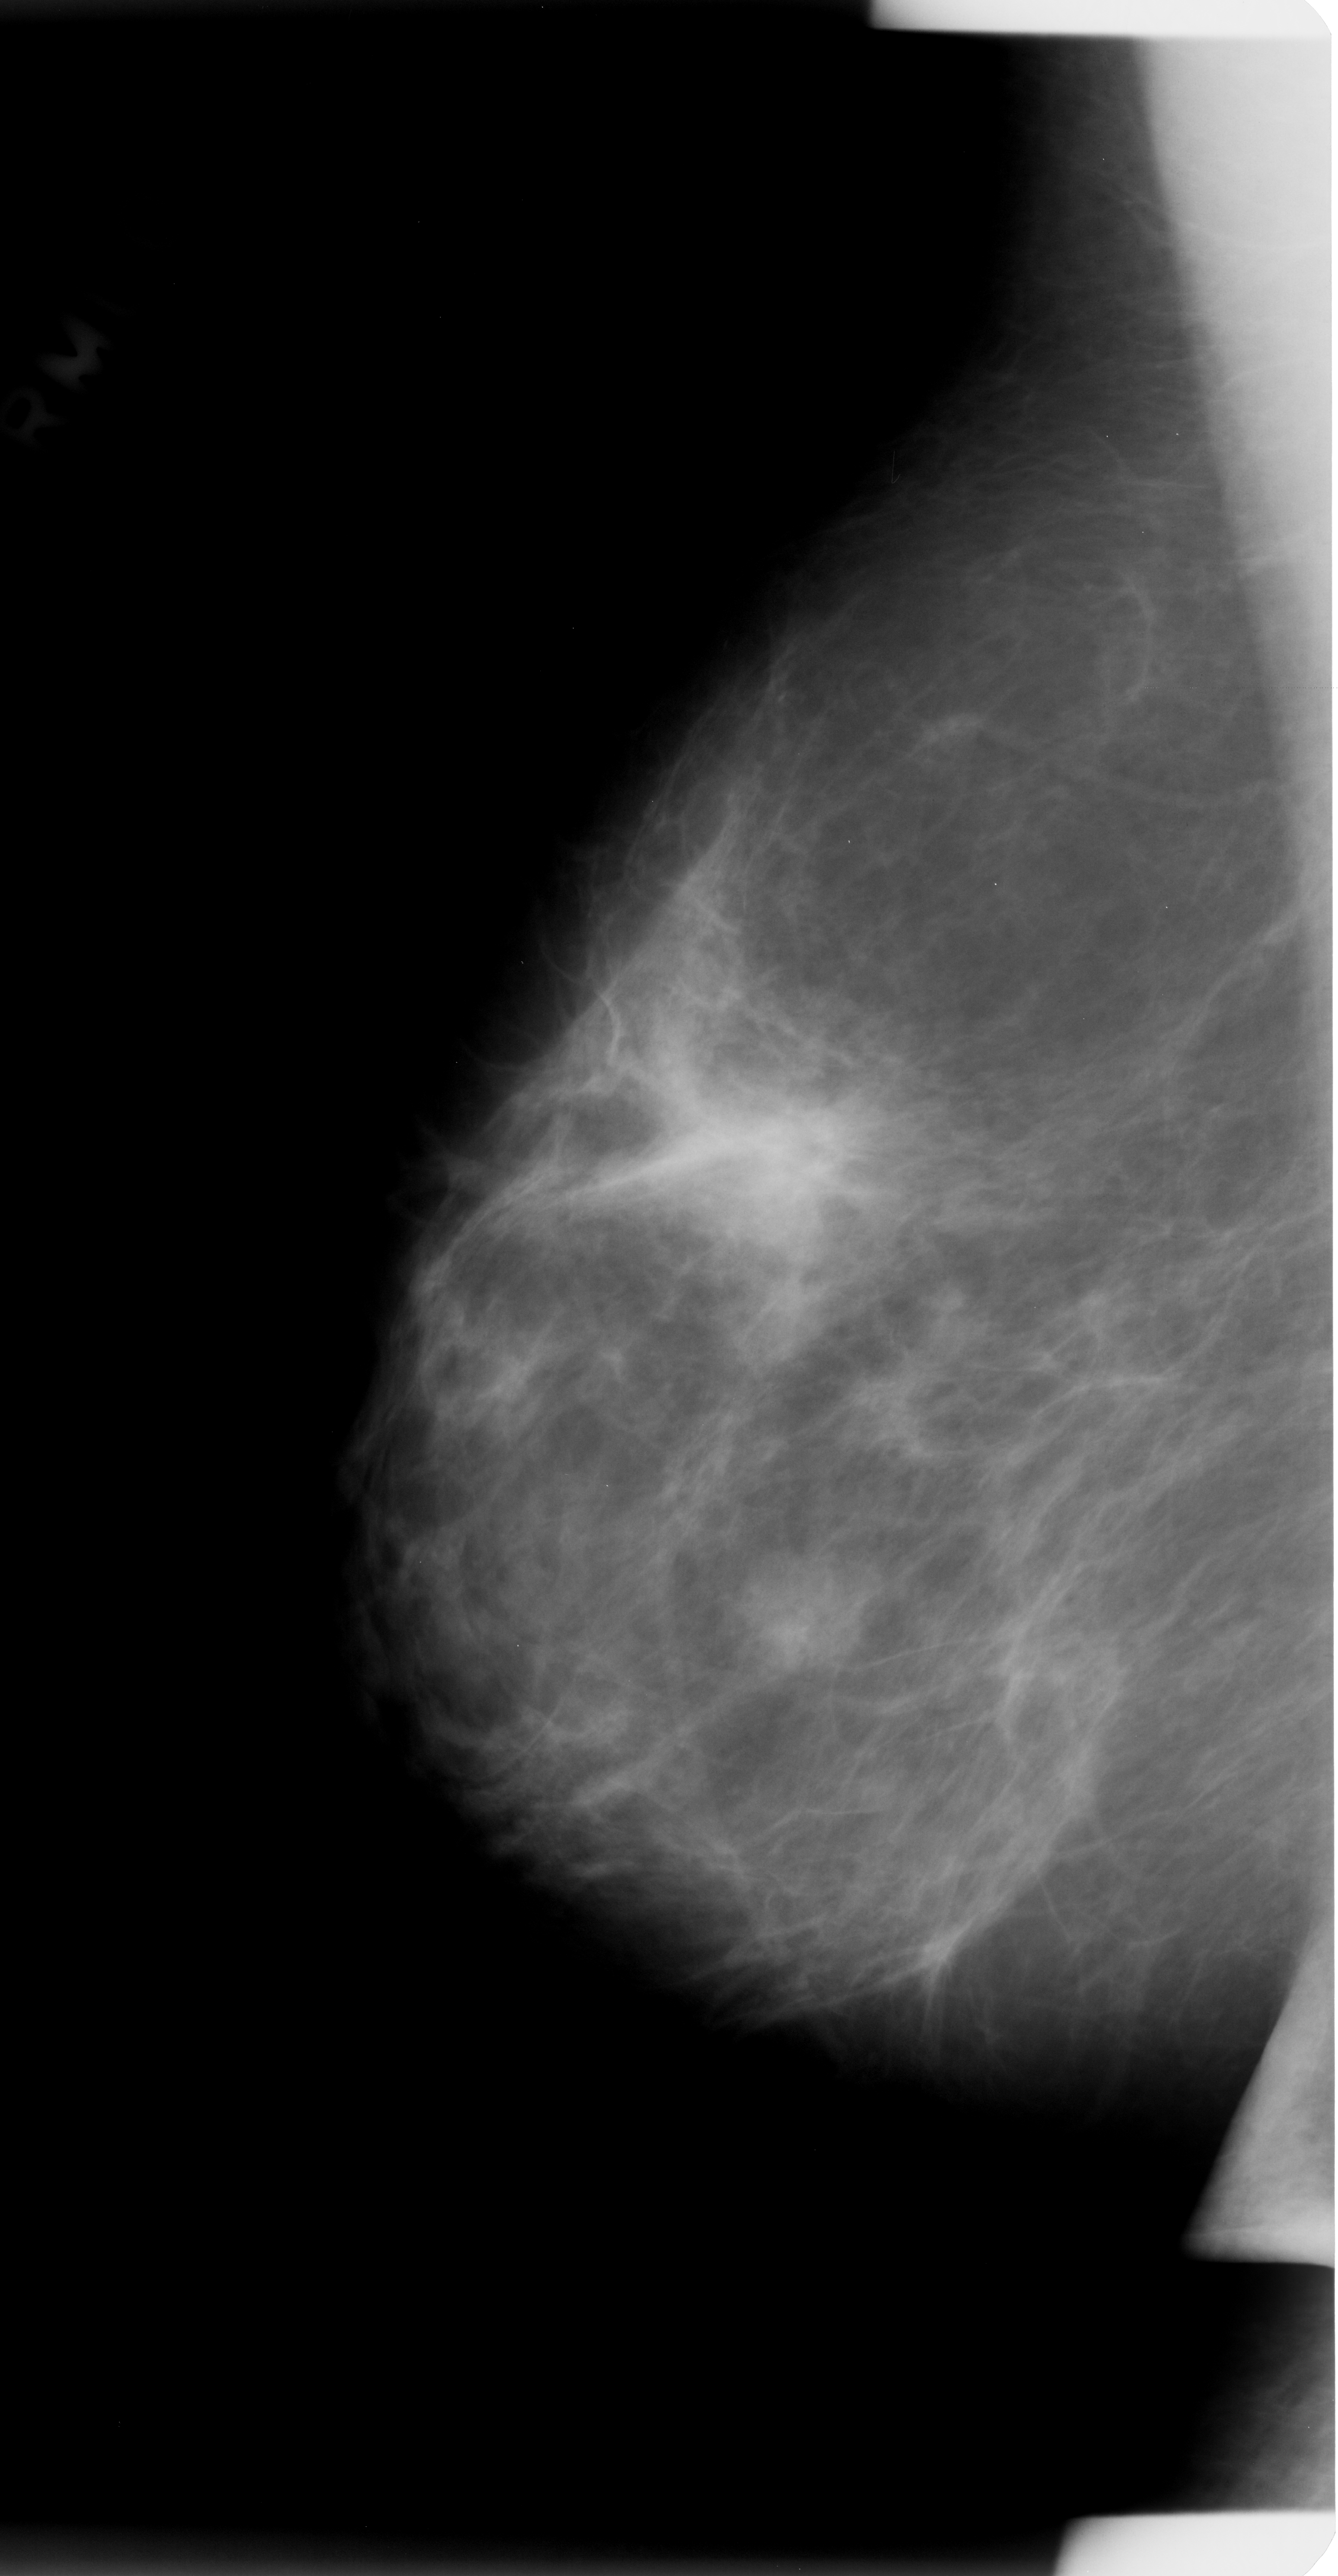
Mammogram (digitized film); right breast; MLO view; BI-RADS breast density category 2 (scale 1–4); 1338 × 2576 image matrix.
Expert-marked regions of interest on this film, with their recorded descriptors:
- mass, shape oval, margins microlobulated; BI-RADS assessment category 4; subtlety rating 3 on a 1 (subtle) to 5 (obvious) scale; pathology (as recorded): benign: box from (x=744, y=1549) to (x=890, y=1681) px